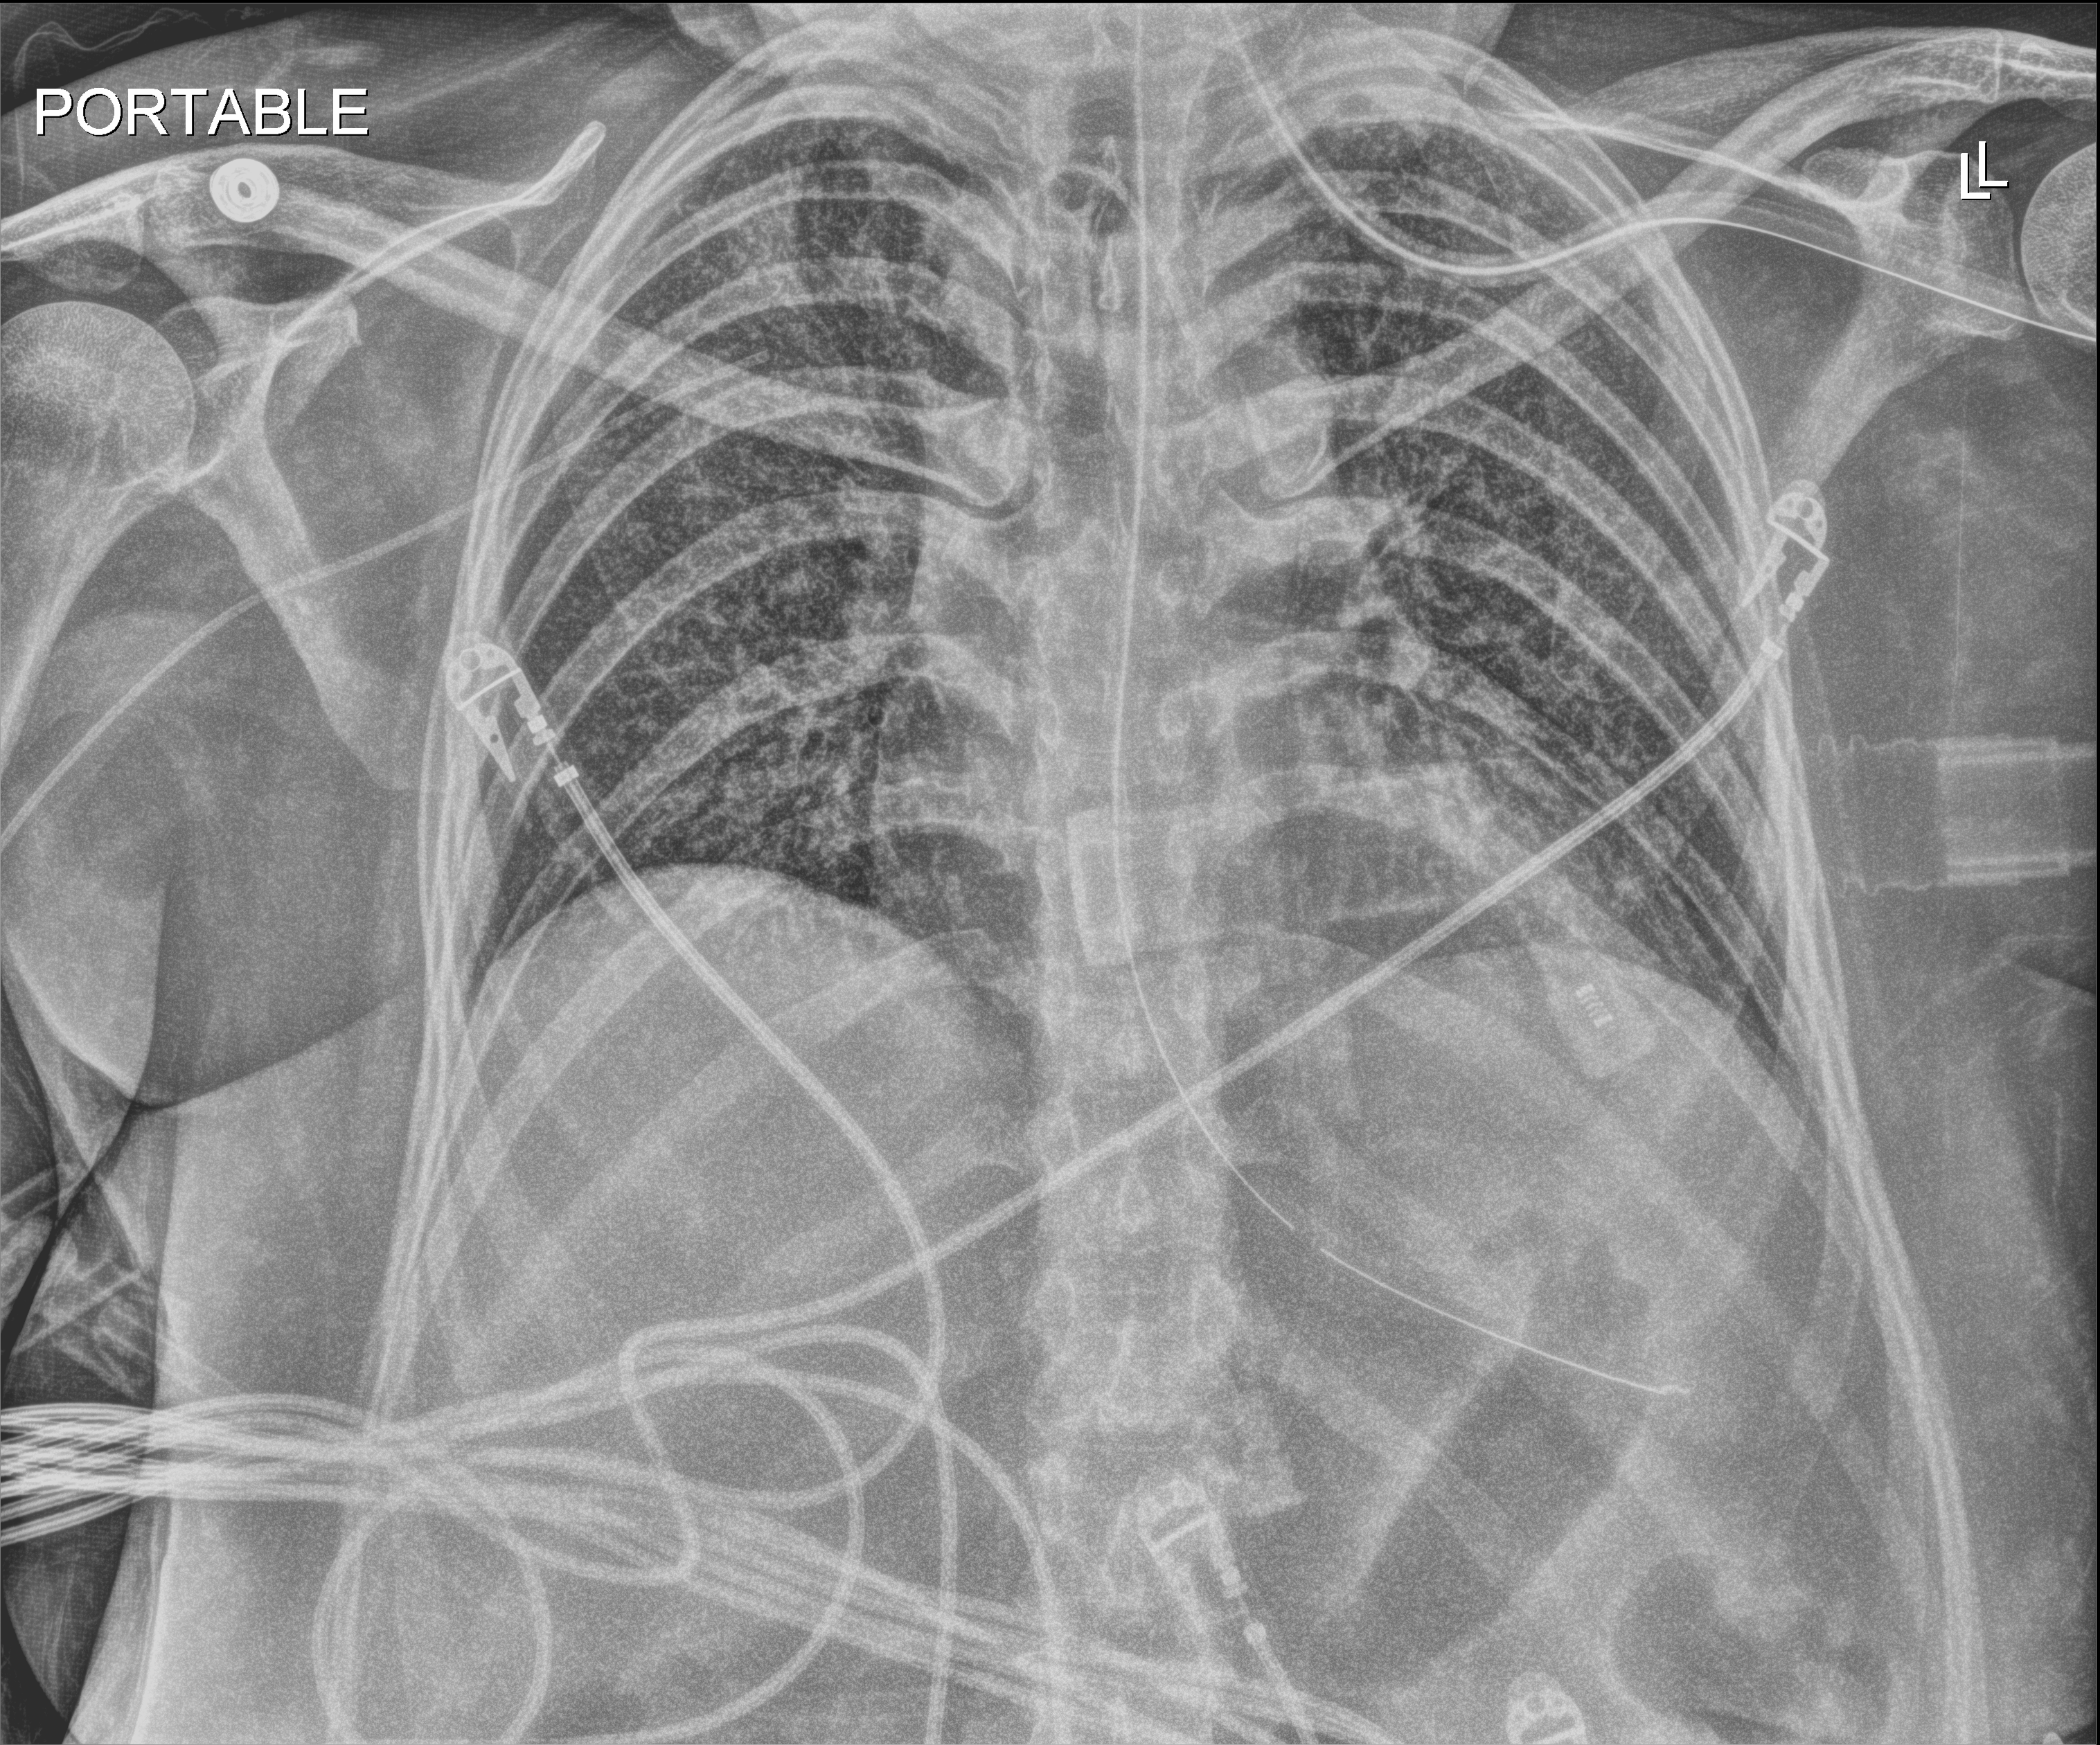
Chest radiograph (digital radiography), anteroposterior (AP) projection. Patient hospitalised with COVID-19; female, aged 18–59 years.
From the hospital-stay record, not from the radiograph (when in the stay this image was taken is not recorded): admitted to intensive care during this hospital stay: yes; length of hospital stay: 73 days.